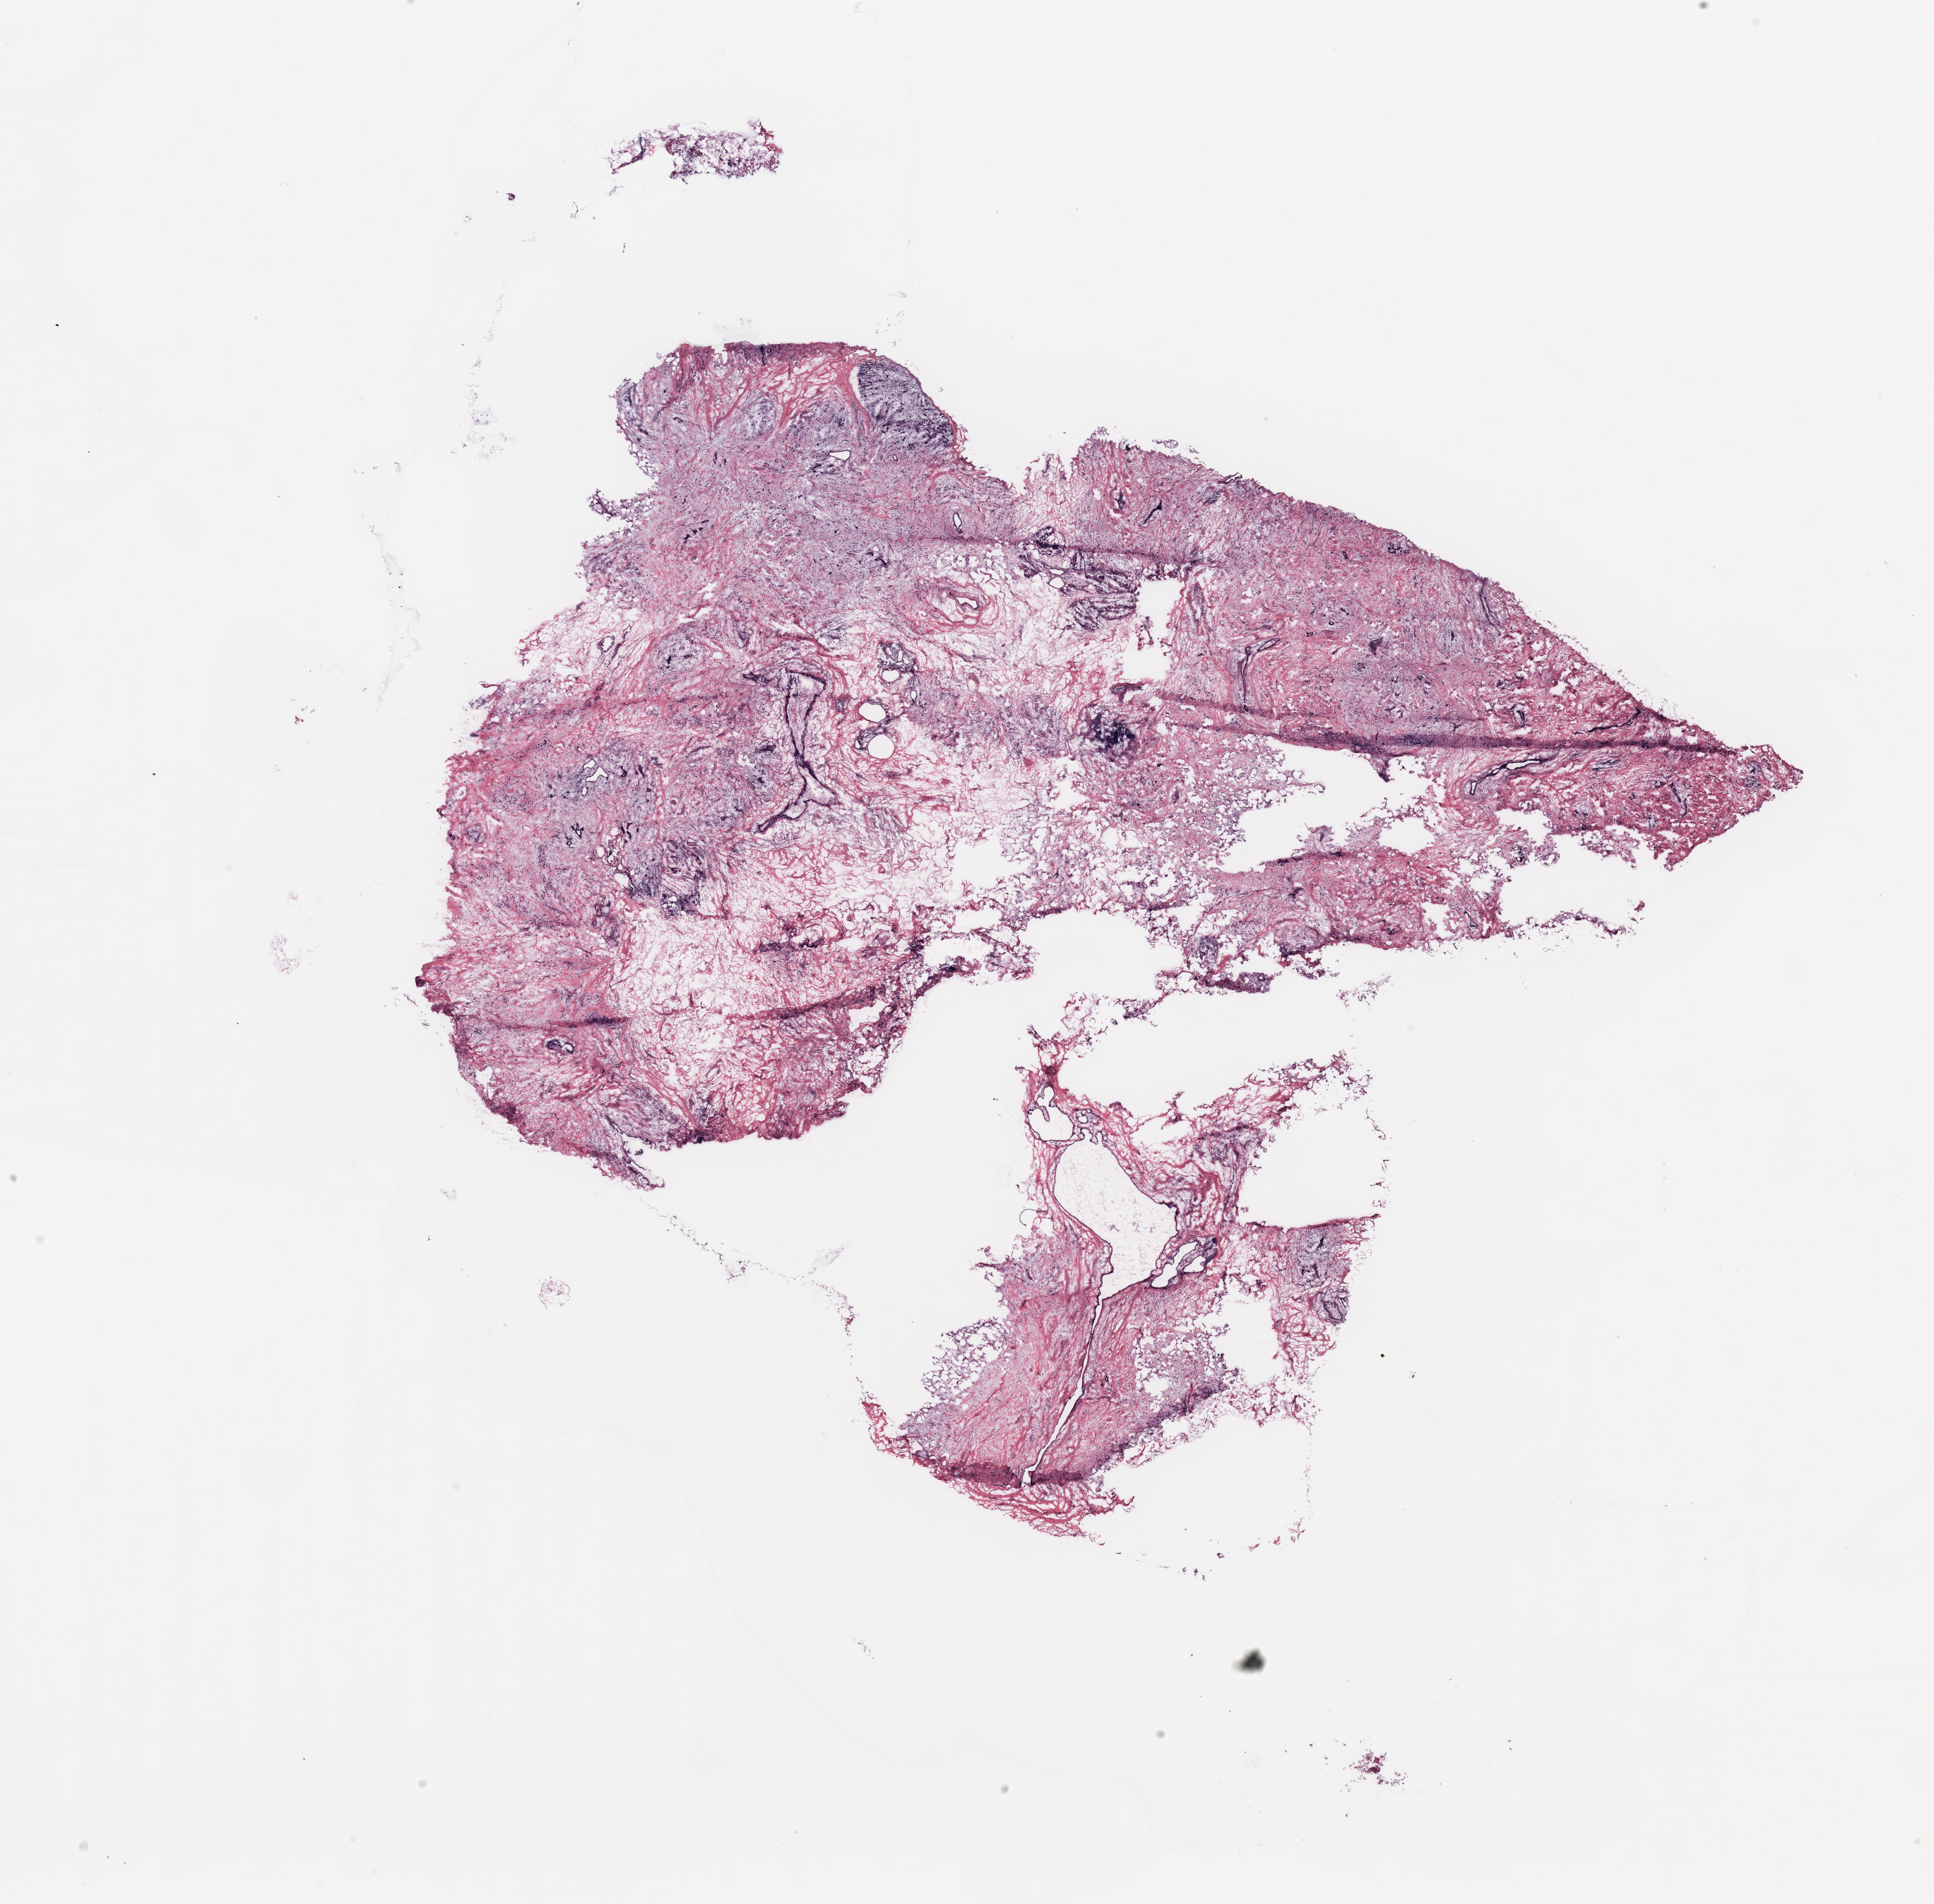
Digitized H&E tissue section (whole slide), shown as a low-resolution overview of the whole scanned area (about 21.7 x 21.3 mm, from a 20x scan). Breast, tissue type not recorded.
Patient diagnosis (cohort enrolment): breast cancer (breast).